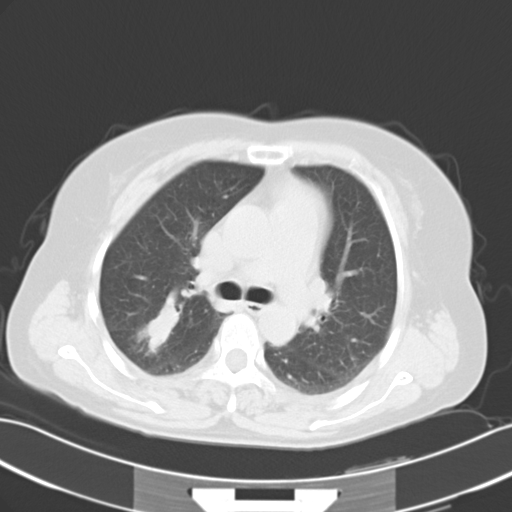
Chest CT, one axial slice. Position 23 of 35 along the scan axis. 120 kVp. Lung window (W 1500 / L -600 HU). 7 mm slice thickness. 512 × 512 image matrix, field of view 353 × 353 mm. Female patient, age 52 years. Case-level facts recorded for this patient, not image findings: clinical TNM (as recorded): T1c N3 M1a.
Annotated regions visible in this slice (rectangle marked by the reading radiologist):
- lung tumour (recorded histology: adenocarcinoma): bounding box [x1, y1, x2, y2] px = [131, 286, 187, 363]